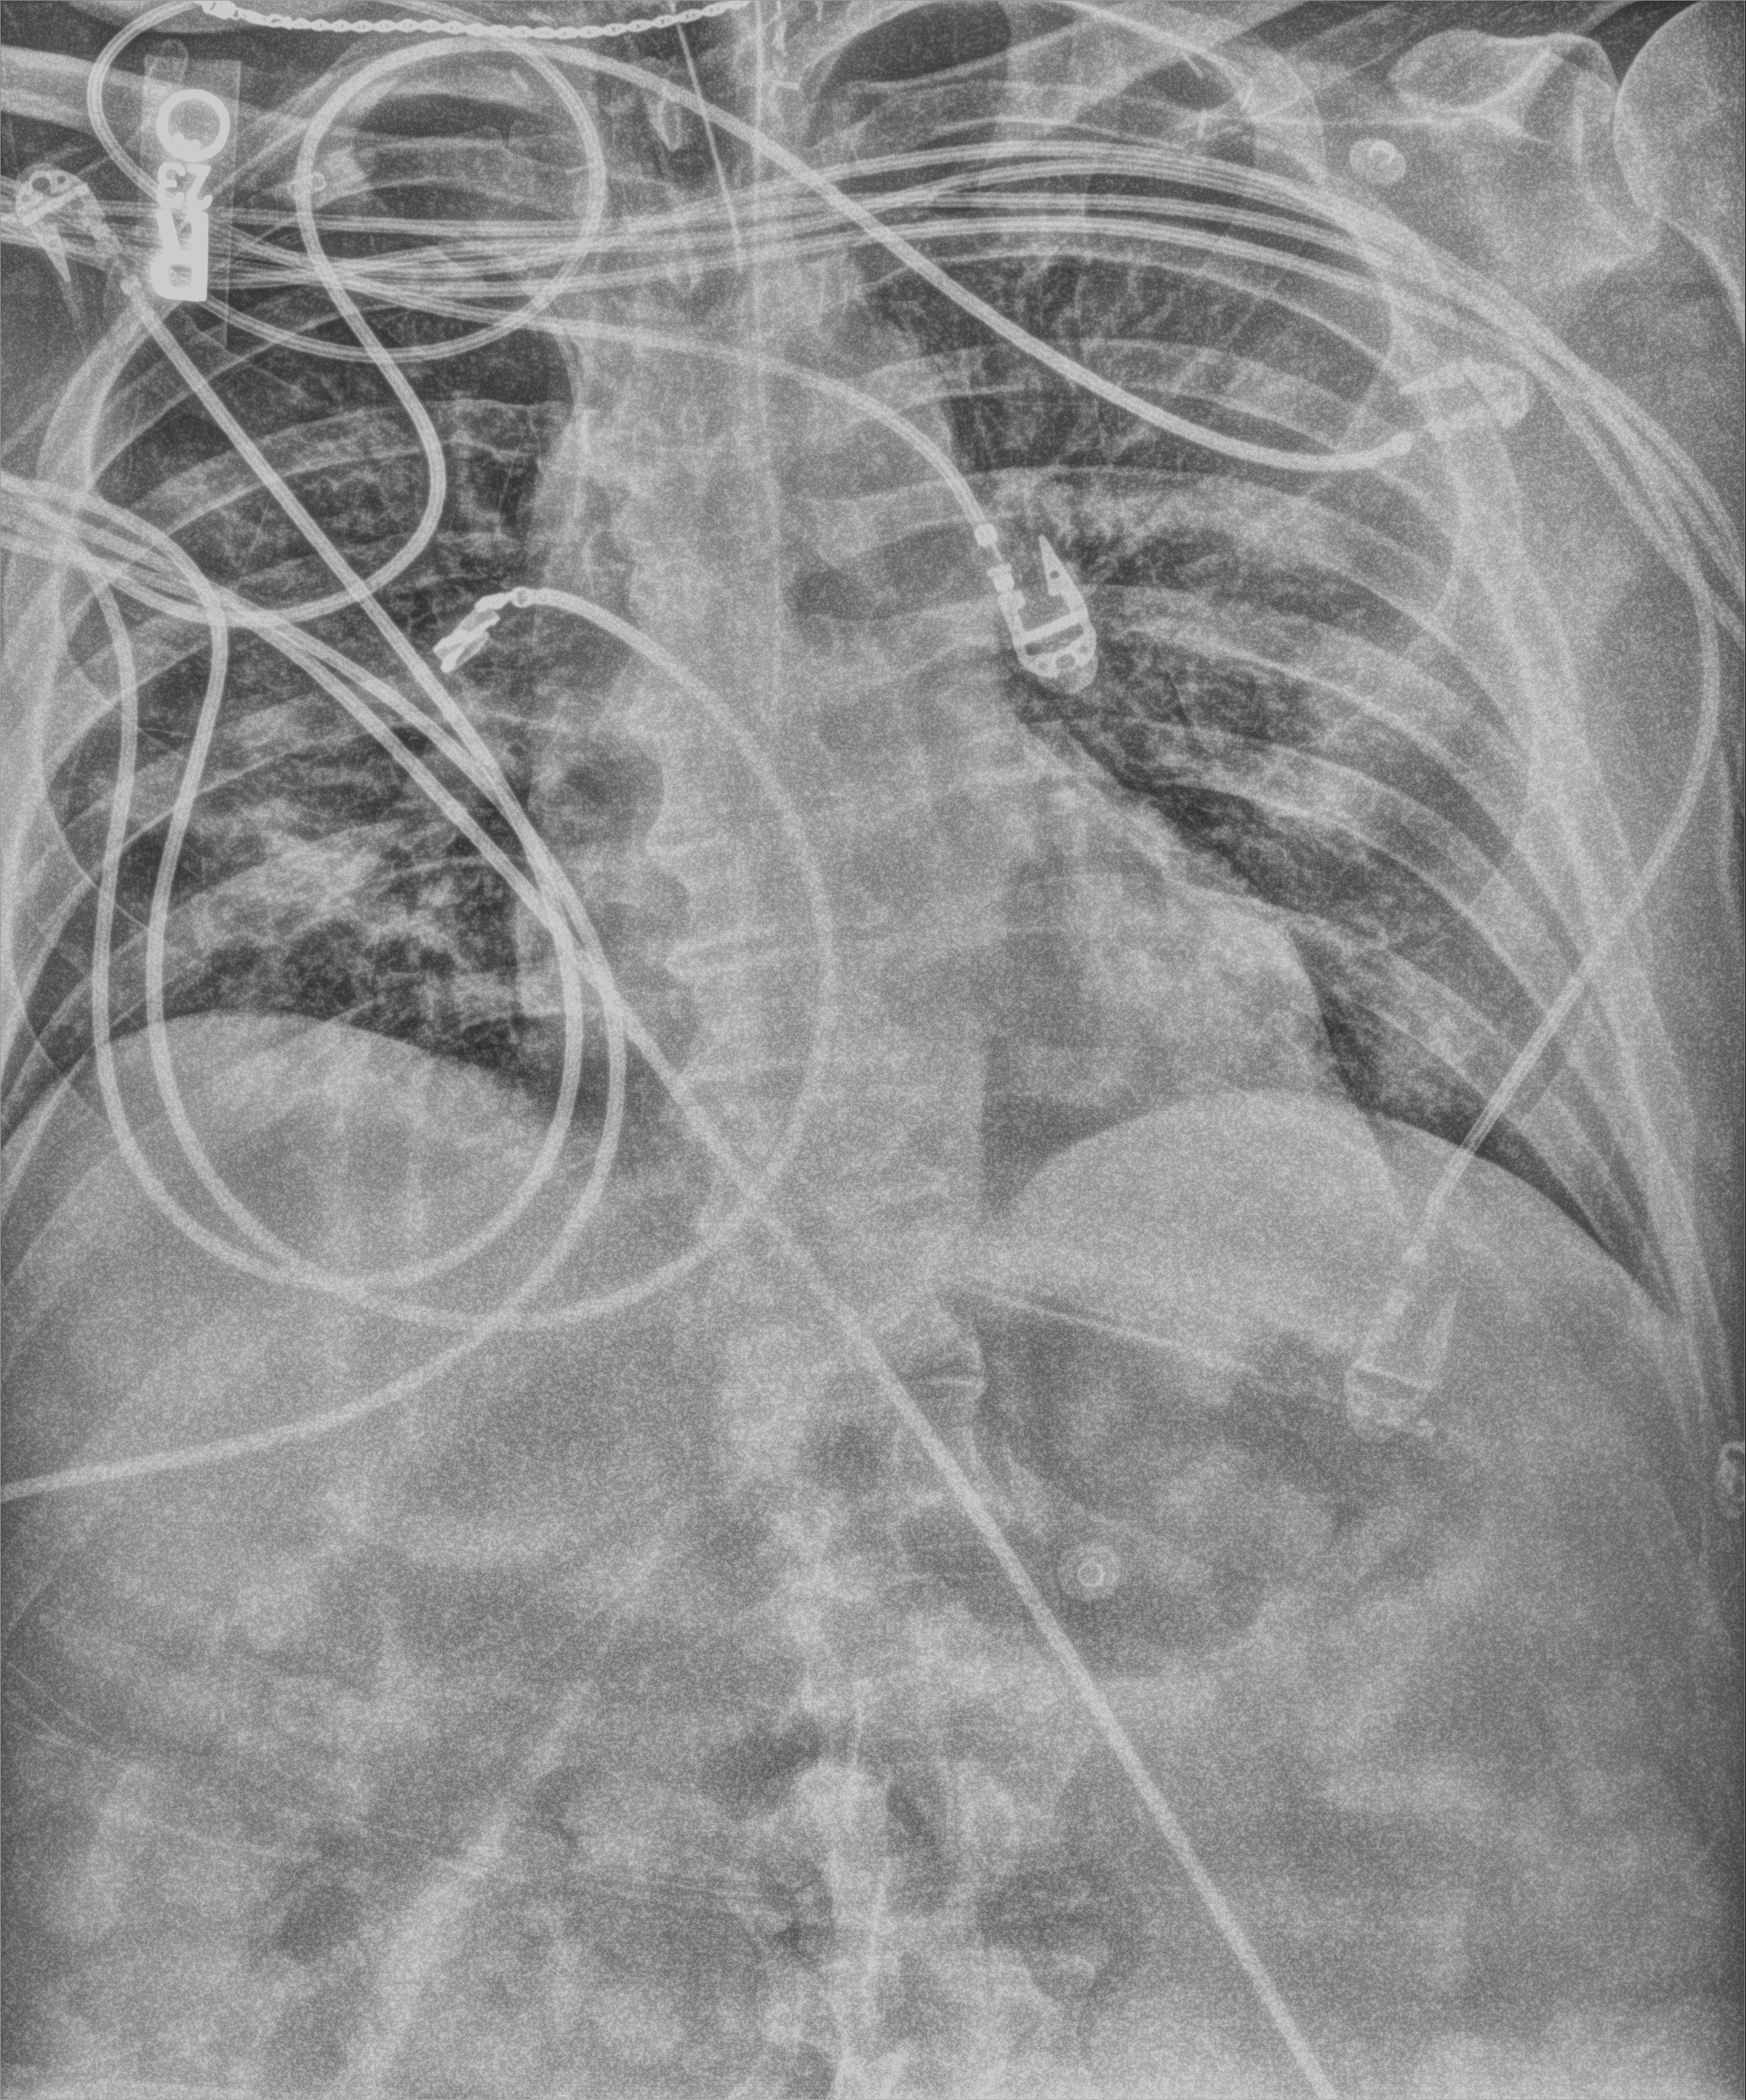
Chest X-ray (portable), anteroposterior (AP) projection. Patient hospitalised with COVID-19, aged 18–59 years.
Hospital-stay facts (about this admission, not read from this image; timing relative to this image not recorded):
- admitted to intensive care during this hospital stay: yes
- chronic kidney disease (admission record): yes